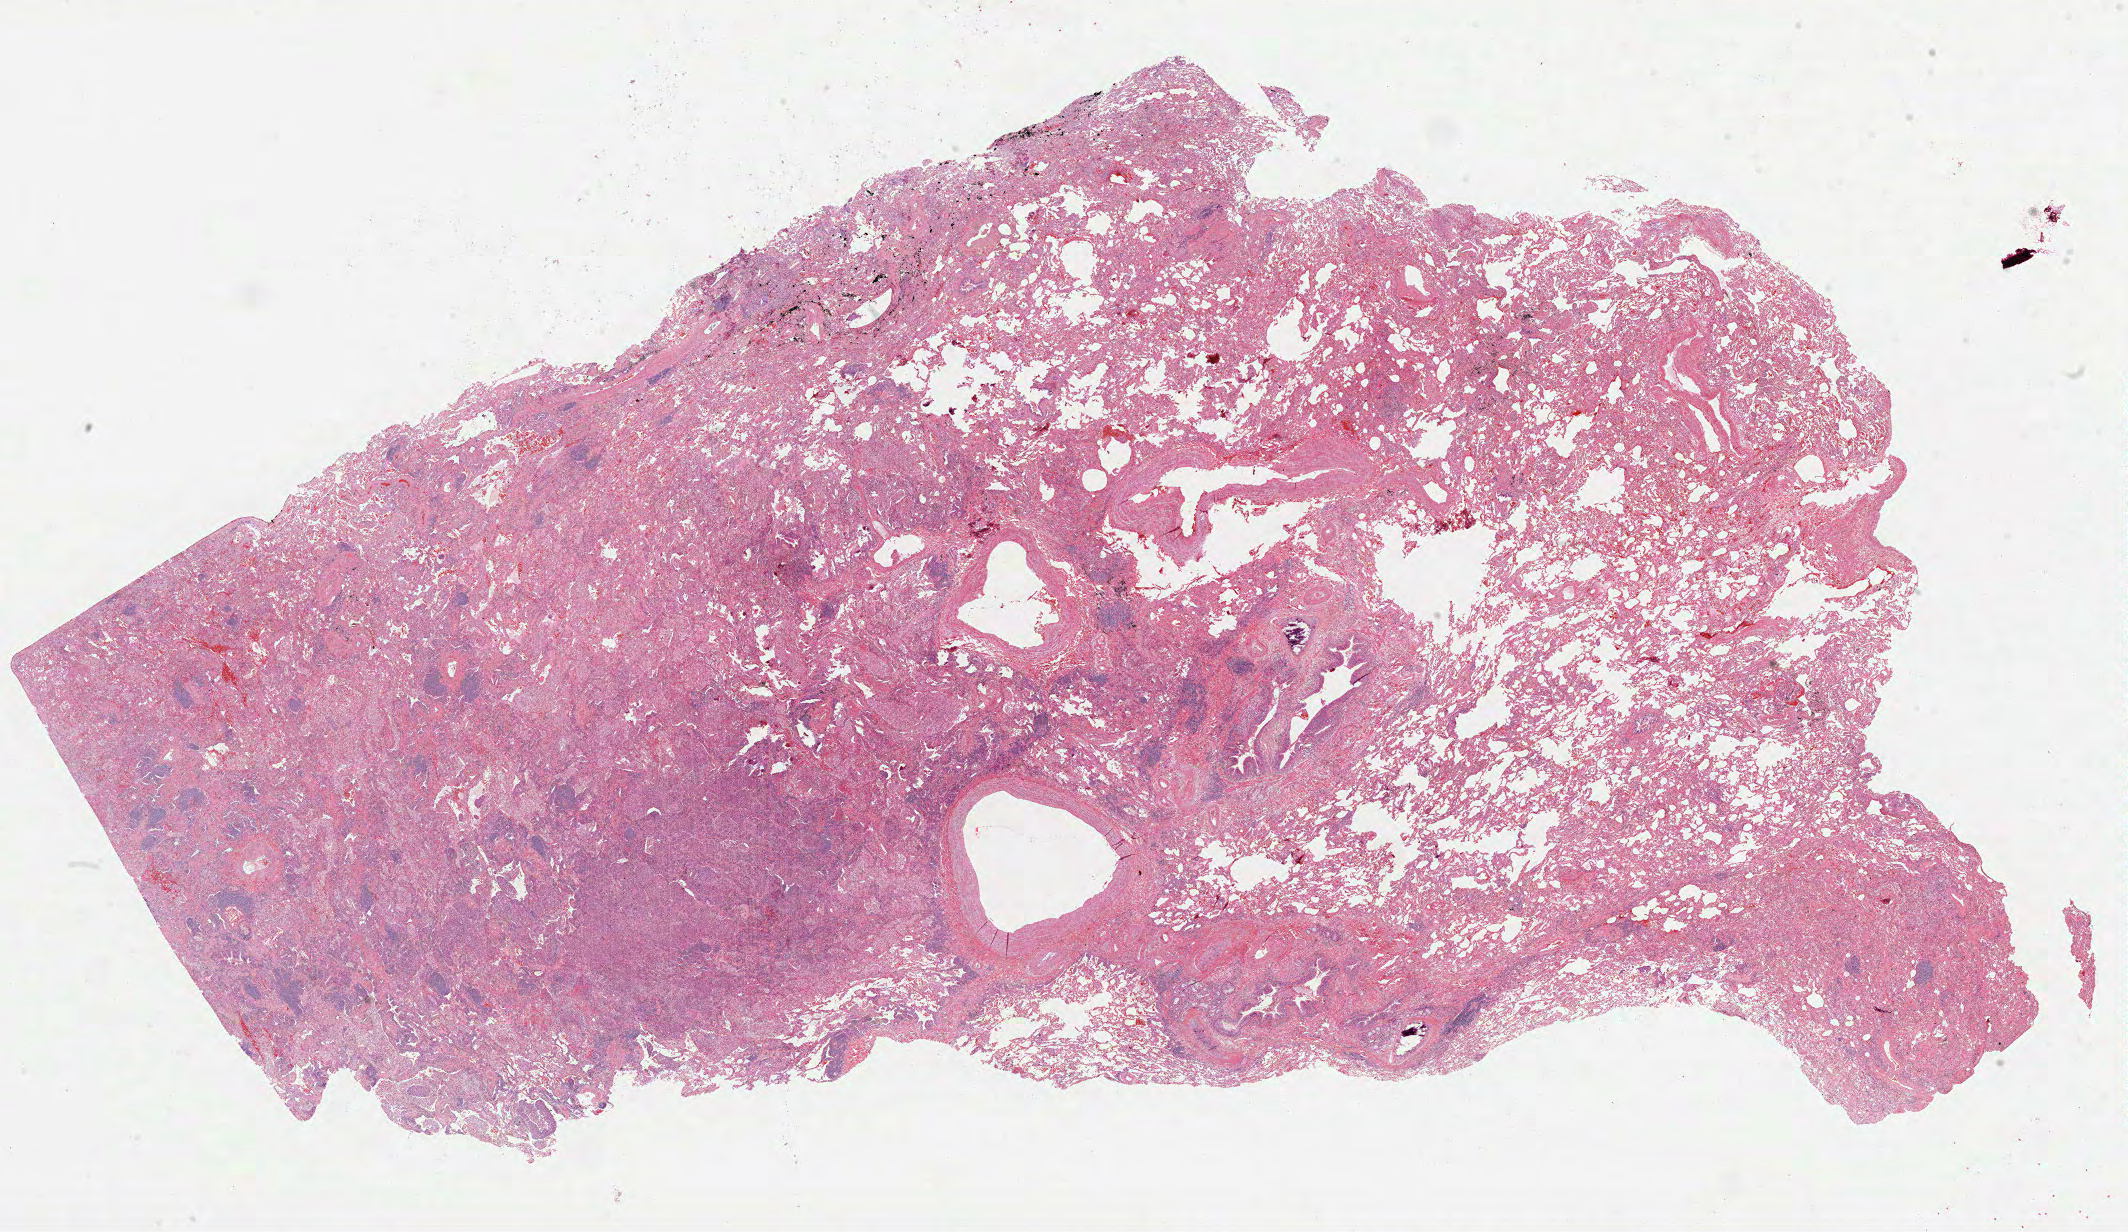
Whole-slide histology image, H&E — shown as a low-resolution overview of the whole scanned area (about 34.3 x 19.9 mm), FFPE section, lung, primary tumour sample. Patient: female, age at initial diagnosis 69 years.
* AJCC pathologic stage: IV
* laterality: left
* histologic diagnosis: Adenocarcinoma, NOS (upper lobe, lung)